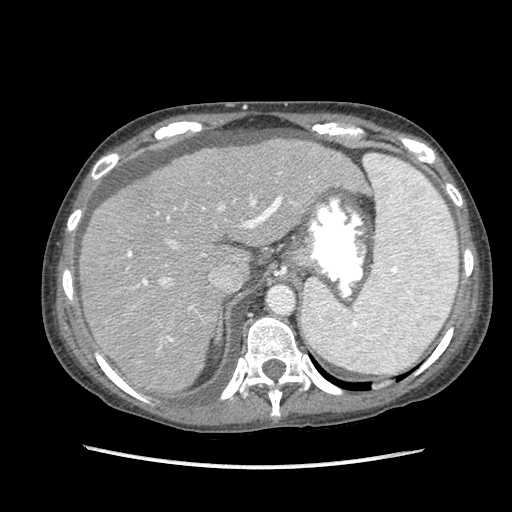
Contrast-enhanced abdominal CT (liver protocol), one axial slice; slice 65 of 87 in the series (ordered by position); reconstruction kernel STANDARD; 120 kVp; soft-tissue window (W 400 / L 40 HU); 2.5 mm slice thickness; 512 × 512 image matrix. Case-level facts recorded for this patient, not image findings: diagnosis: hepatocellular carcinoma (patient treated with transarterial chemoembolisation; whether this scan precedes or follows treatment is not stated here); TNM stage (as recorded): Stage-IIIB; Child-Pugh class: A; tumour nodularity: uninodular.
Outlined on this slice (semi-automatic segmentation, software-assisted and operator-edited):
- abdominal aorta: bounding box <269,286,293,314> (left, top, right, bottom; pixels)
- liver parenchyma outside the tumour (the mass and vessels are separate outlines, so this box may not span the whole liver): <80,138,365,393>
- liver vessels: <127,172,315,351>